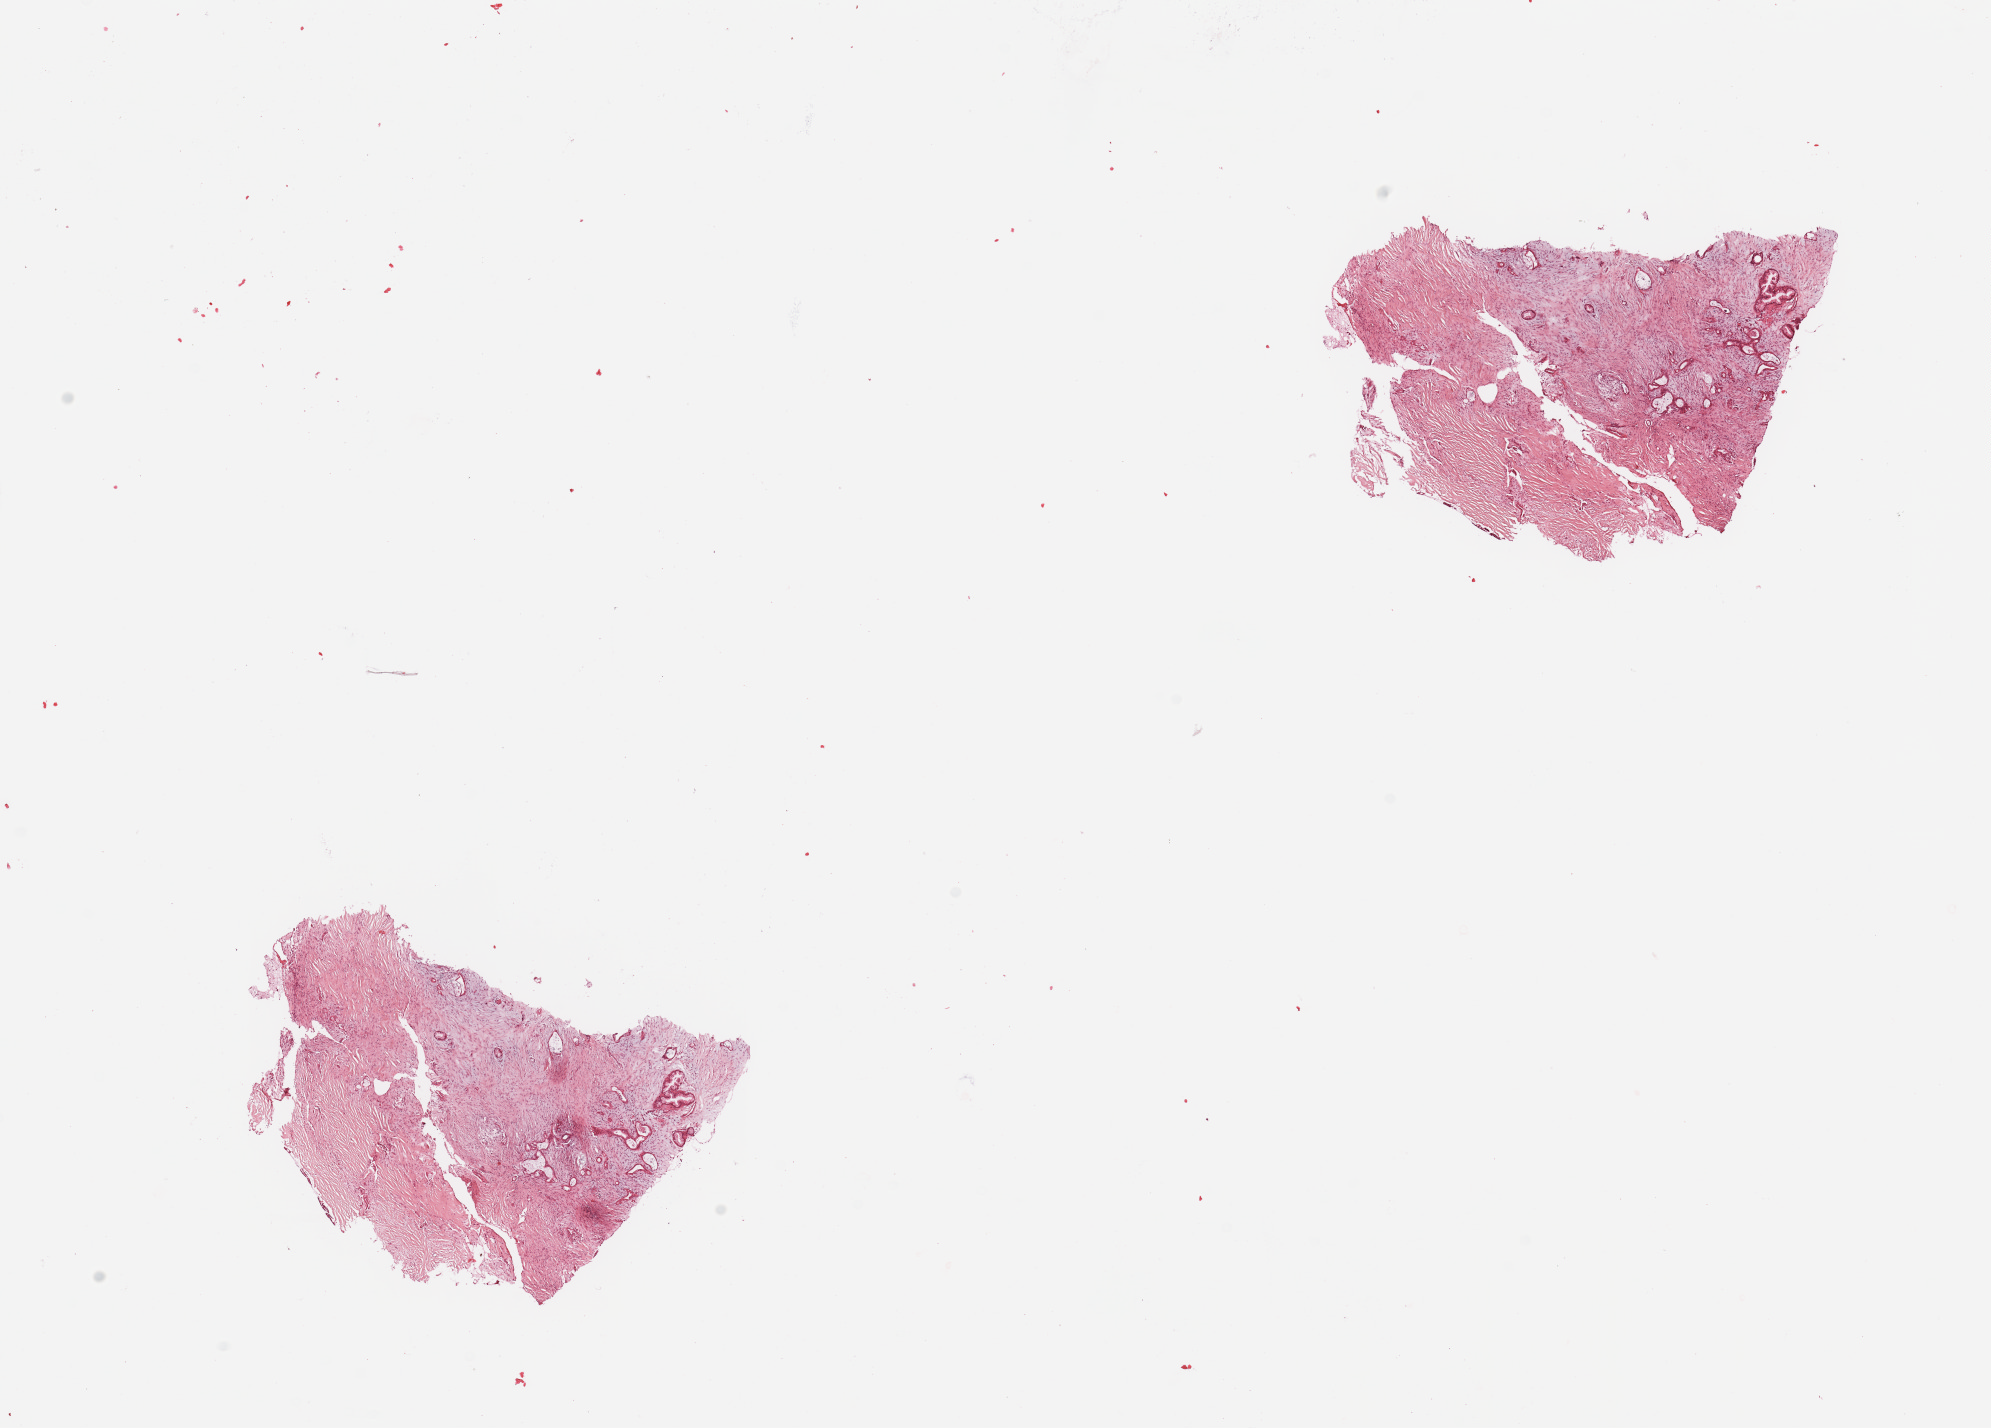
Digitized H&E-stained tissue section (whole slide), low-resolution overview of the scanned area, about 15.8 x 11.3 mm (slide scanned at 20x); tumour tissue sample, sampled site: pancreas. 69-year-old male patient. Histologic grade: G3 (poorly differentiated). Composition of this section per pathologist review: tumour nuclei 10%, necrosis 2%.
AJCC pathologic stage: IIB. Primary tumour site (as recorded): head. Diagnosis: Infiltrating duct carcinoma, NOS.